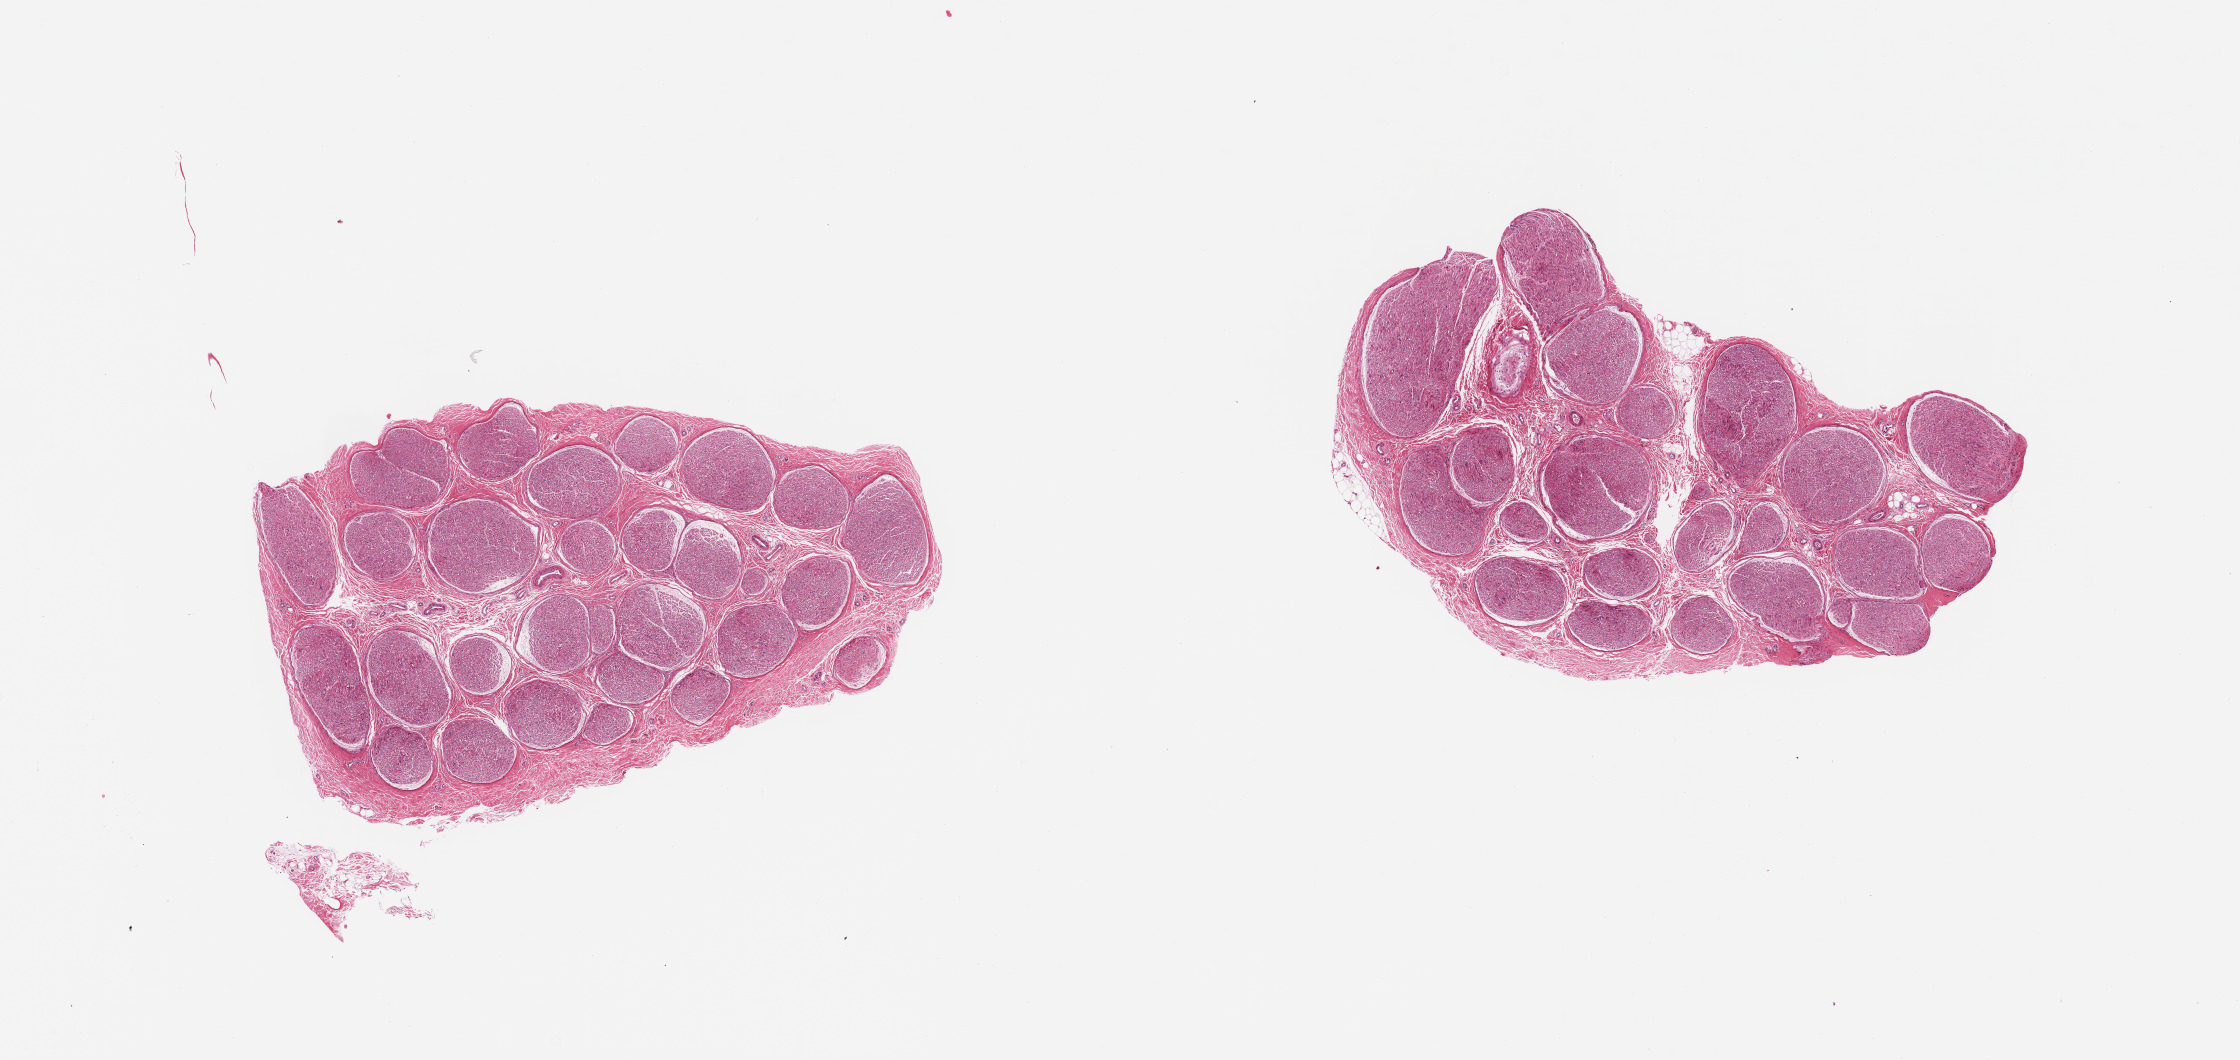
Digitized H&E-stained section, whole scanned area (about 17.7 x 8.4 mm) shown as a low-resolution overview. PAXgene-fixed, paraffin-embedded tissue. Sampled site (target tissue): tibial nerve. Tissue donor sample. Donor sex: male.
• review note (as recorded): 2 pieces, no significant adherent fat